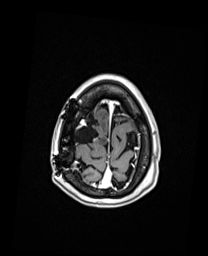
Brain MRI from a brain-tumour surgery series, one axial slice. T1-weighted post-contrast. 1 mm slice thickness. 208 × 256 image matrix. From the clinical record (not read from this slice): histopathology: Oligodendroglioma; WHO grade: 3; IDH mutation: yes; tumour location: Right Frontal.
Structures marked on this image (manually delineated by an expert):
- previous resection cavity: bounding box <72,114,95,143> (left, top, right, bottom; pixels)